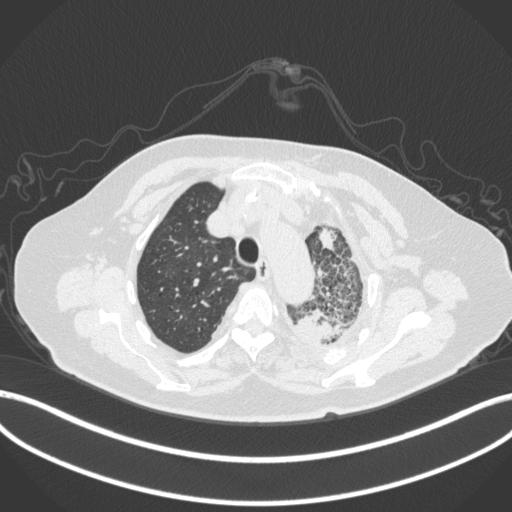
Chest CT, one axial slice. Position 313 of 399 along the scan axis. 120 kVp. Lung window (W 1500 / L -600 HU). 1 mm slice thickness. 512 × 512 image matrix, field of view 400 × 400 mm. Patient: female, 75 years. Case-level facts recorded for this patient, not image findings: clinical TNM (as recorded): T3 N3 M1.
Annotated regions visible in this slice (bounding box drawn by a radiologist):
- lung tumour (recorded histology: adenocarcinoma): bounding box <292,303,339,344> (left, top, right, bottom; pixels)